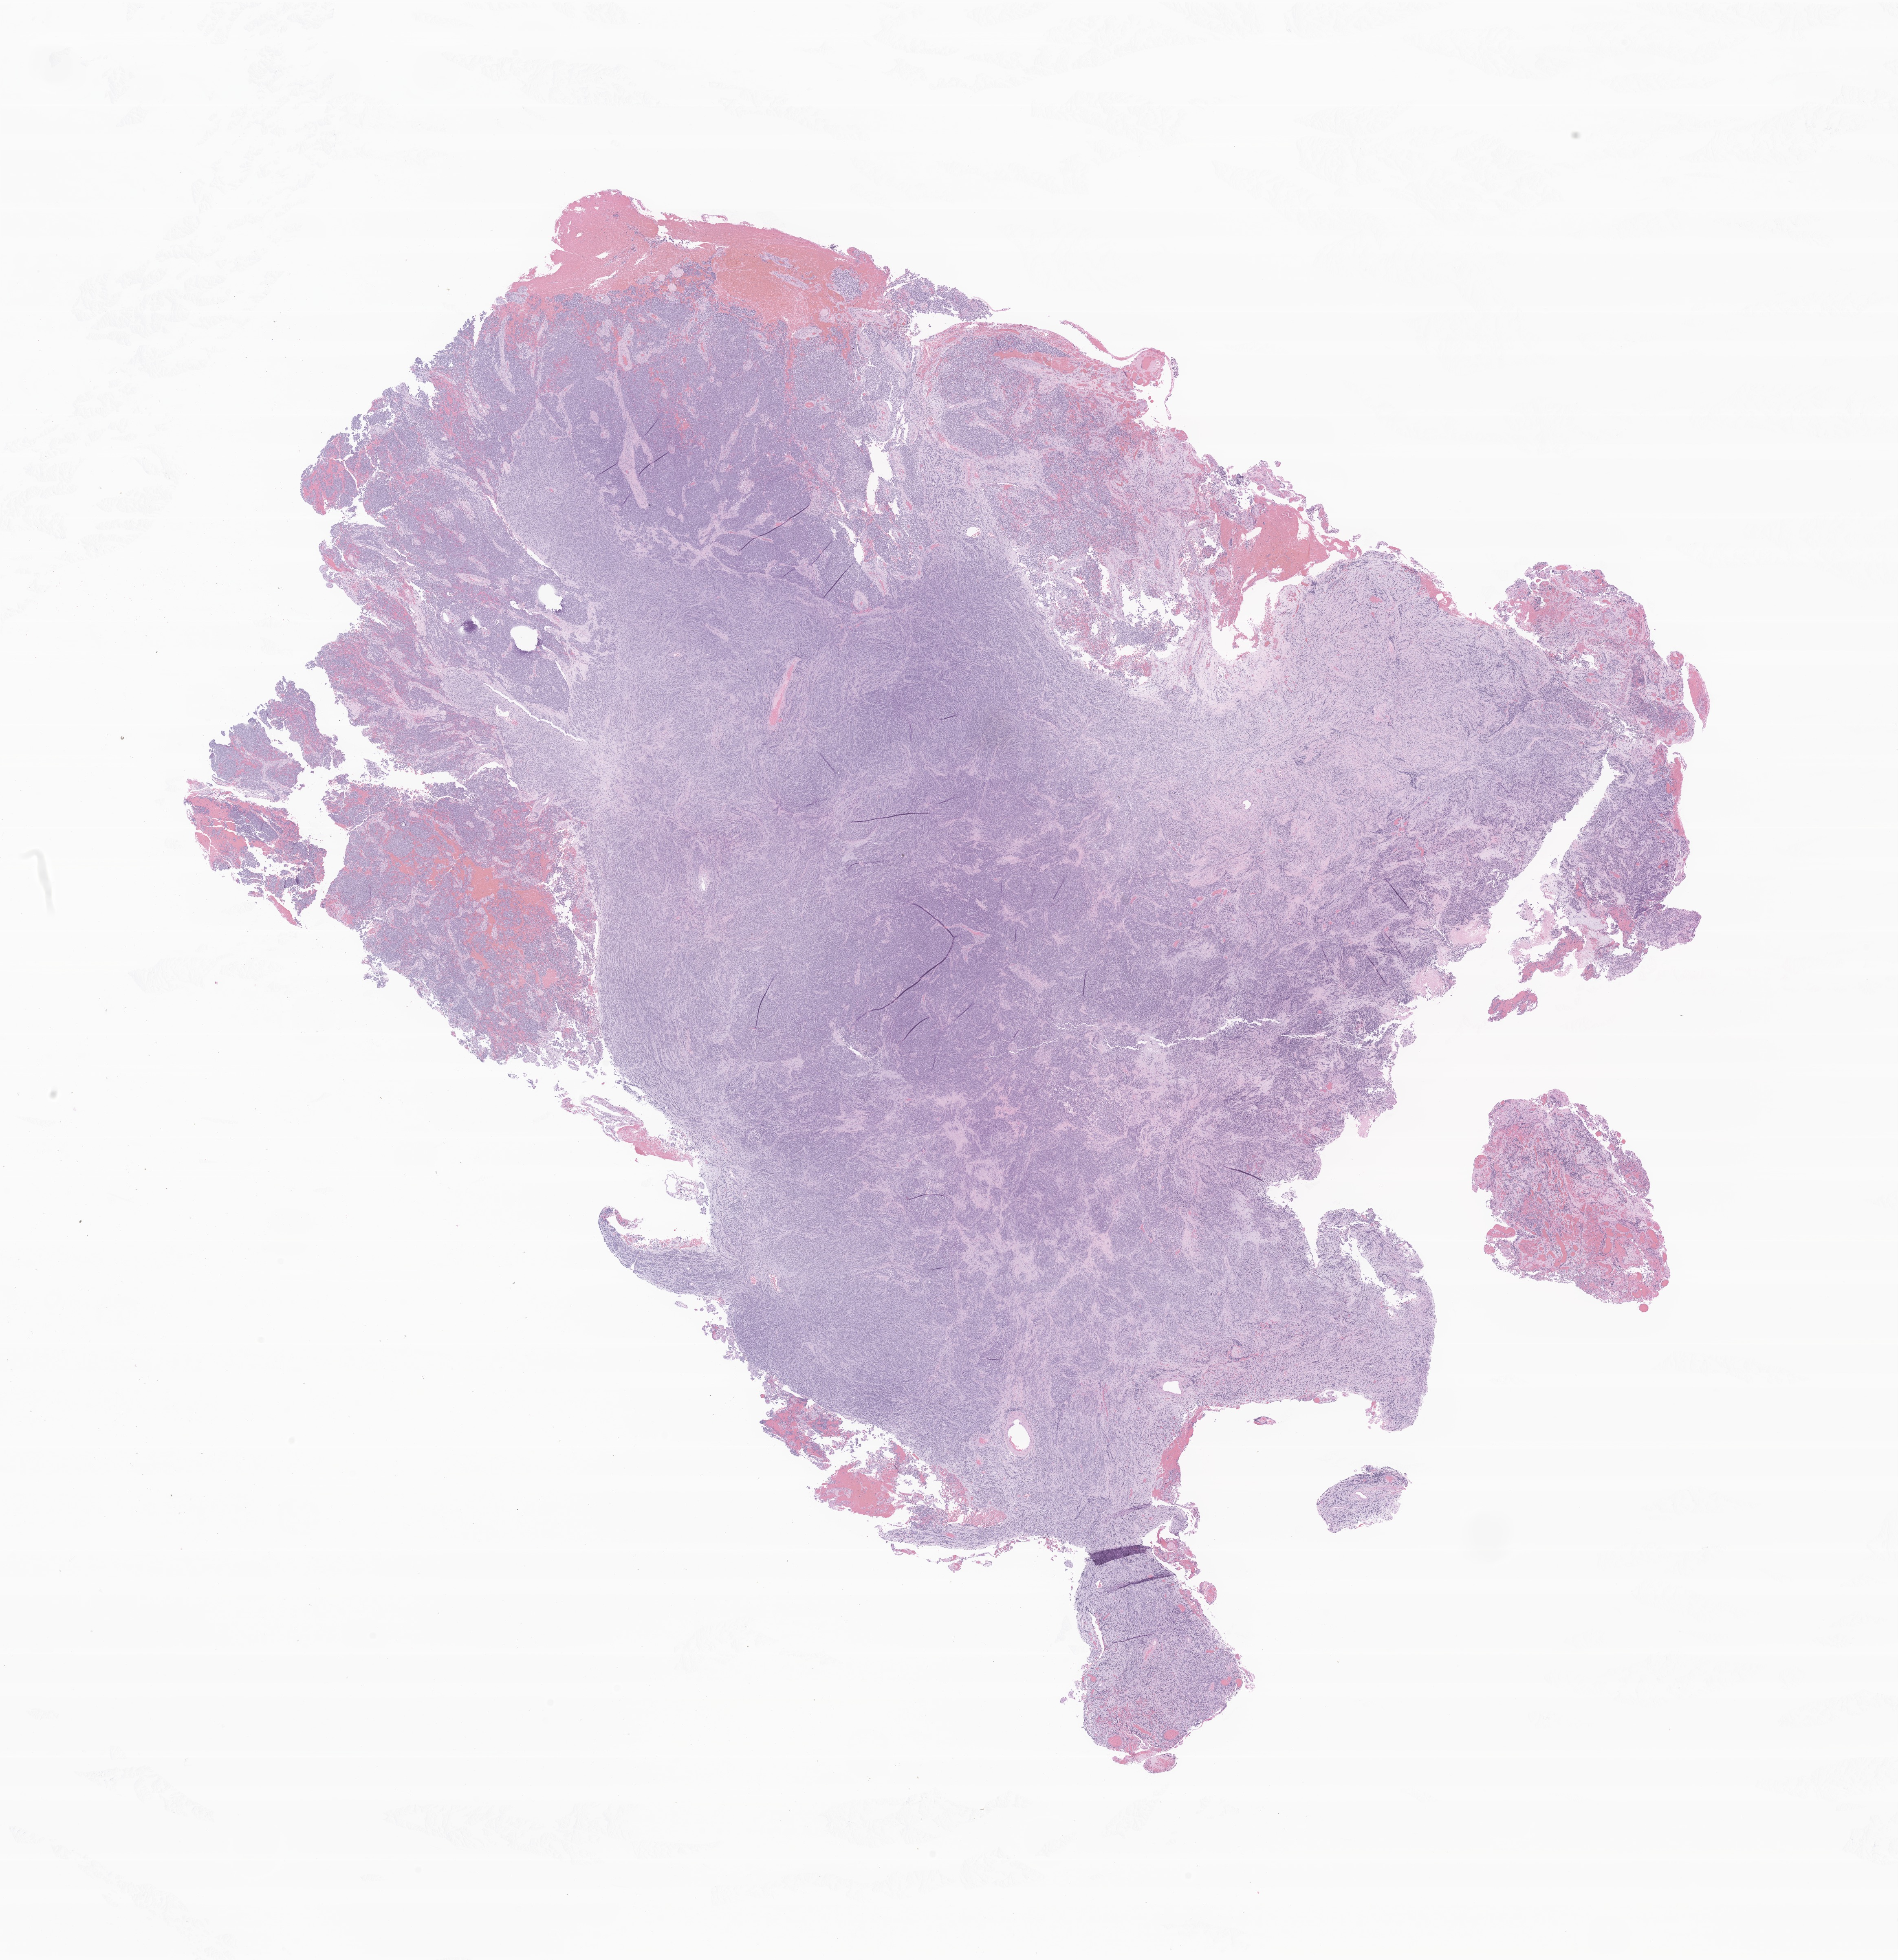
Whole-slide image, hematoxylin and eosin (H&E) stain of tumor tissue from the brain — shown as a low-resolution overview of the whole scanned area (about 19.6 x 20.3 mm); FFPE section. Male patient, age 112 months (9 years 4 months).
Diagnosis (ICD-O-3 morphology term): Medulloblastoma, NOS.